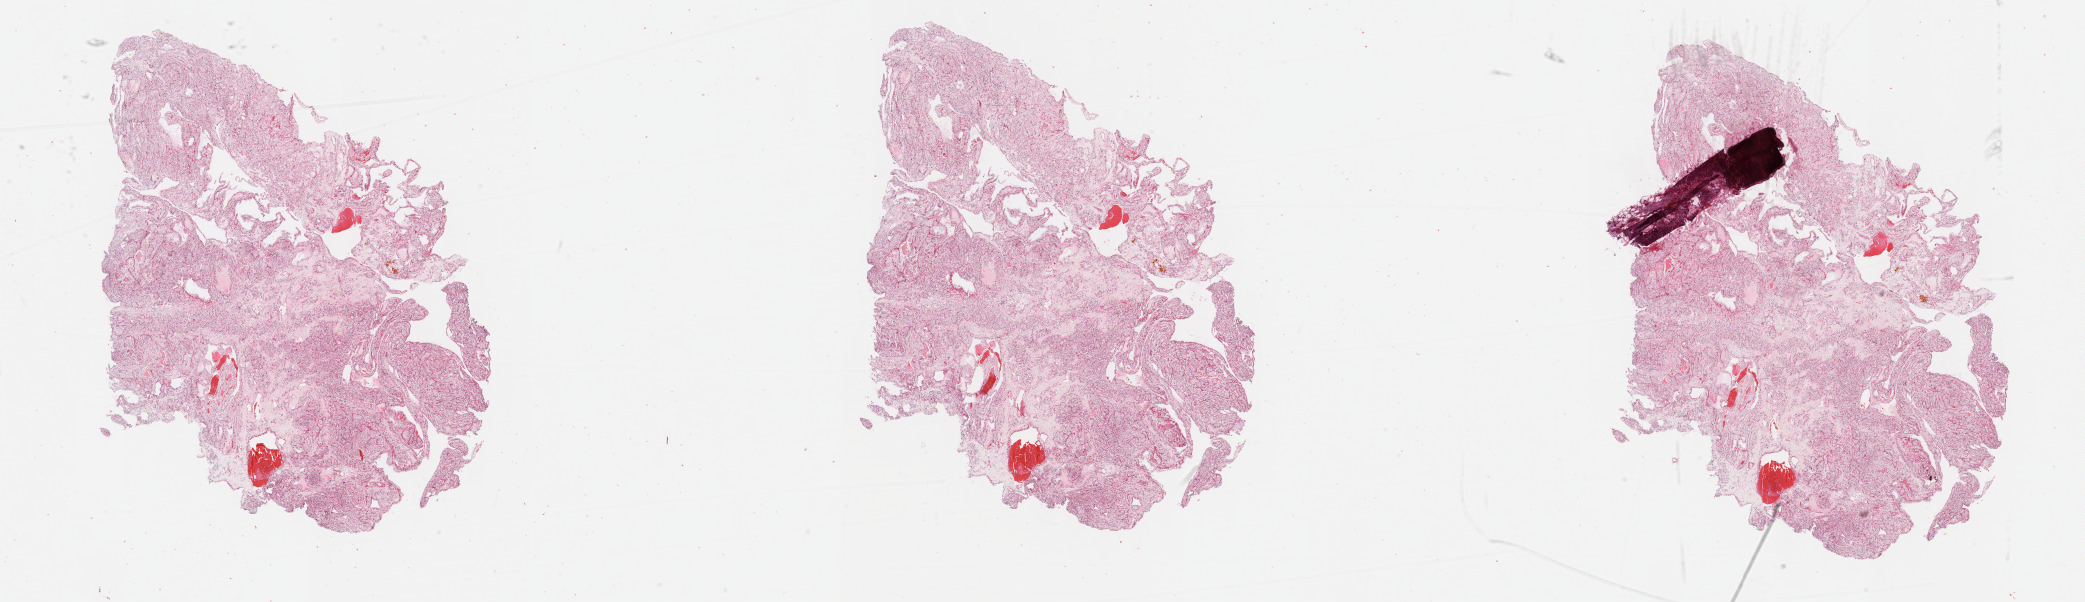
Whole-slide histology image, Hematoxylin and eosin (H&E) stained, low-resolution overview of the scanned area, about 33.7 x 9.7 mm (slide scanned at 40x), formalin-fixed paraffin-embedded (FFPE) diagnostic section, primary tumour sample from the kidney. Male patient; age at initial diagnosis 35 years. Histologic grade: G1 (well differentiated).
Pathologic diagnosis: Clear cell adenocarcinoma, NOS. AJCC pathologic stage: I (7th edition).